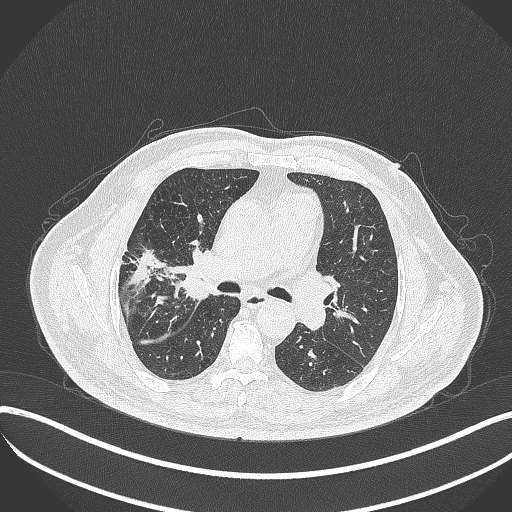
Chest CT, one axial slice; slice 214 of 401 in the series (ordered by position); reconstruction kernel B70f; 120 kVp; lung window (W 1500 / L -600 HU); 1 mm slice thickness; 512 × 512 image matrix. Patient: male, 72 years. Case-level facts recorded for this patient, not image findings: clinical TNM (as recorded): T1c N0 M0.
Structures marked on this image (bounding box drawn by a radiologist):
- lung tumour (recorded histology: squamous cell carcinoma): bounding box (x1, y1, x2, y2) in pixels: (162, 239, 211, 307)